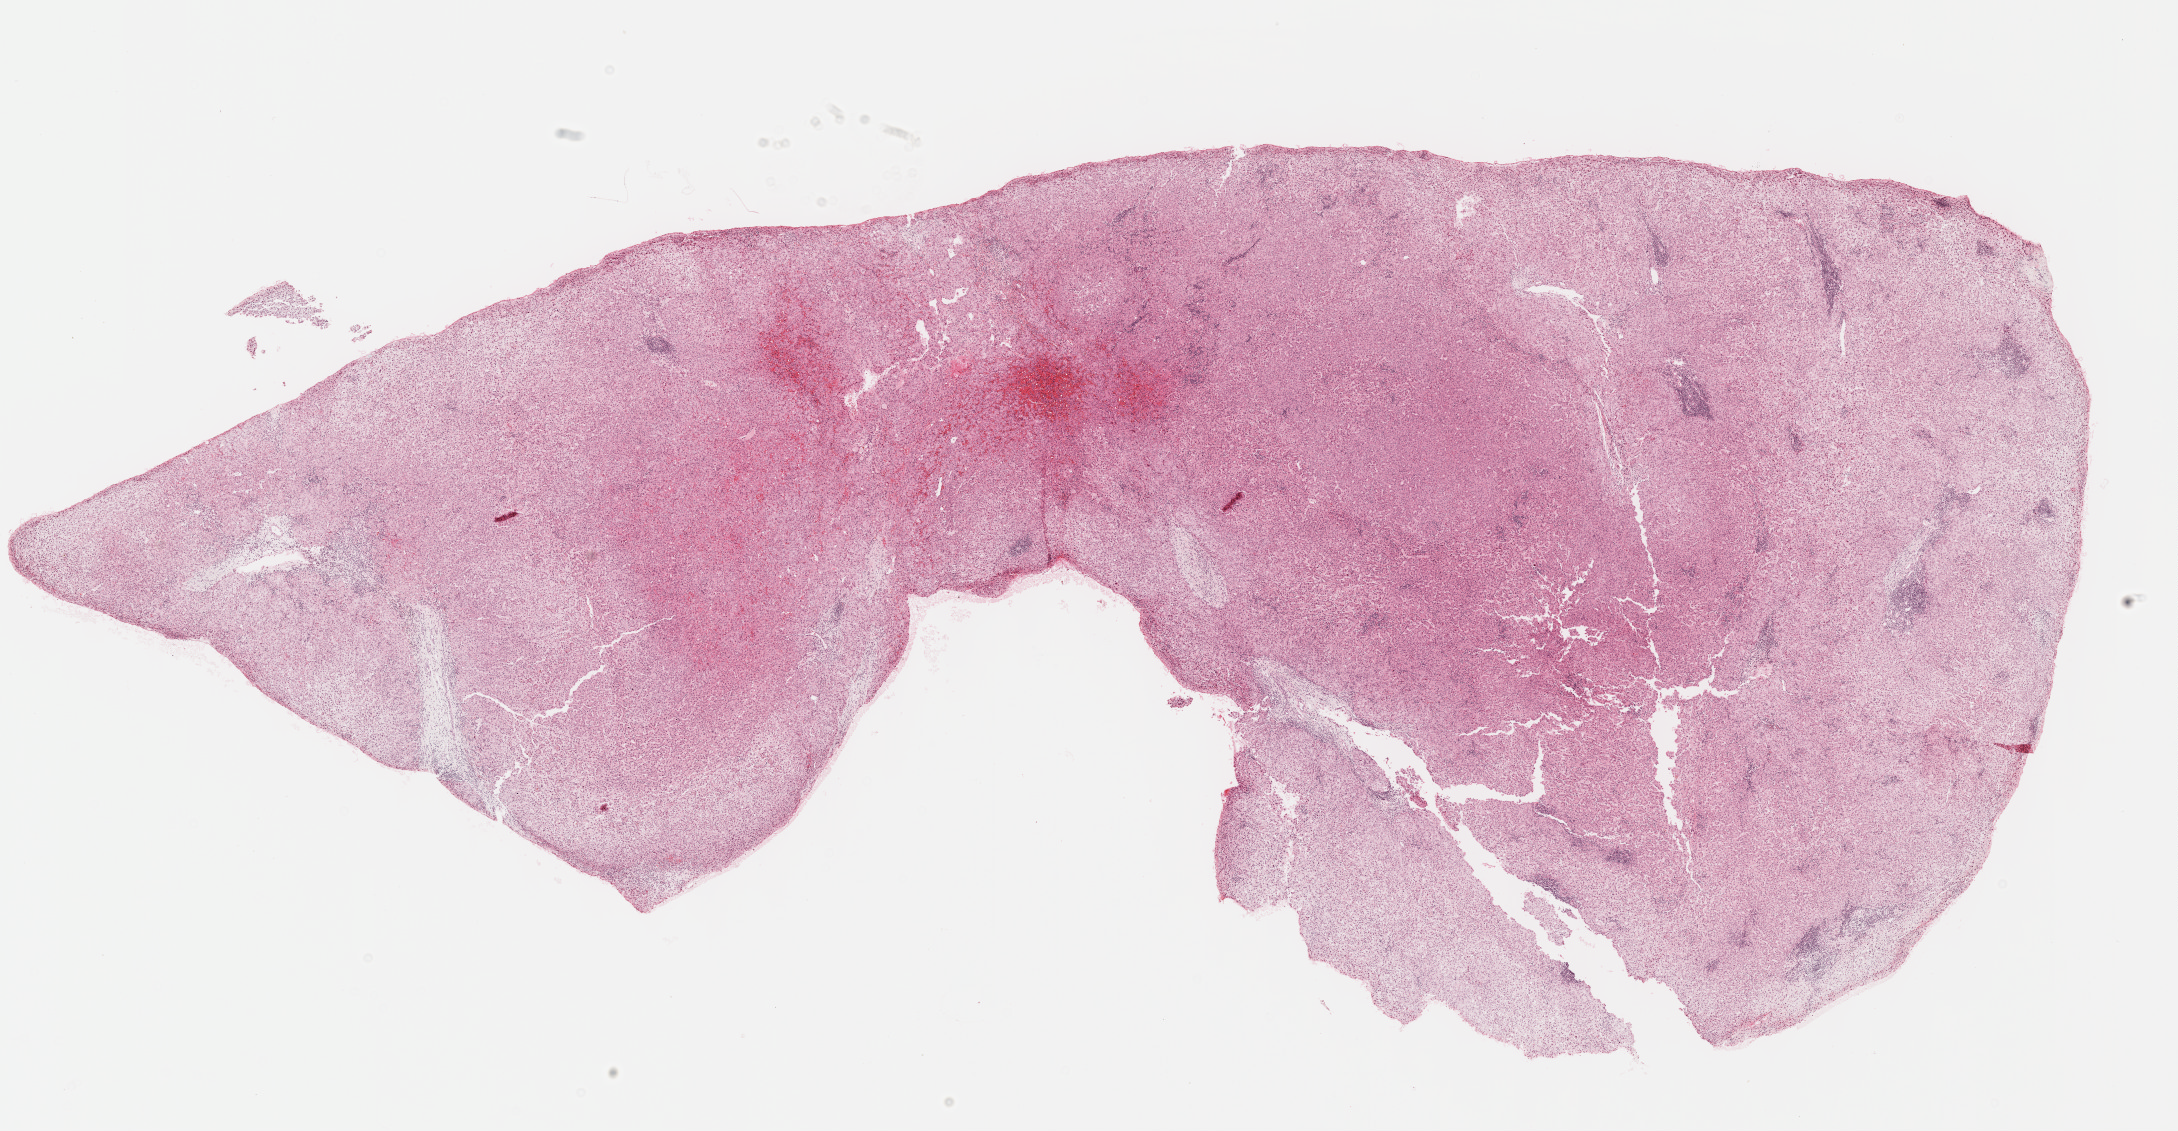
Hematoxylin and eosin (H&E) stained whole-slide image, a low-resolution overview of the entire scanned area, about 17.6 x 9.1 mm. FFPE section. Liver, primary tumour sample. Male, age 72 years at initial diagnosis. Histologic grade: G2 (moderately differentiated).
AJCC pathologic stage: I (7th edition). Diagnosis: Hepatocellular carcinoma, NOS.